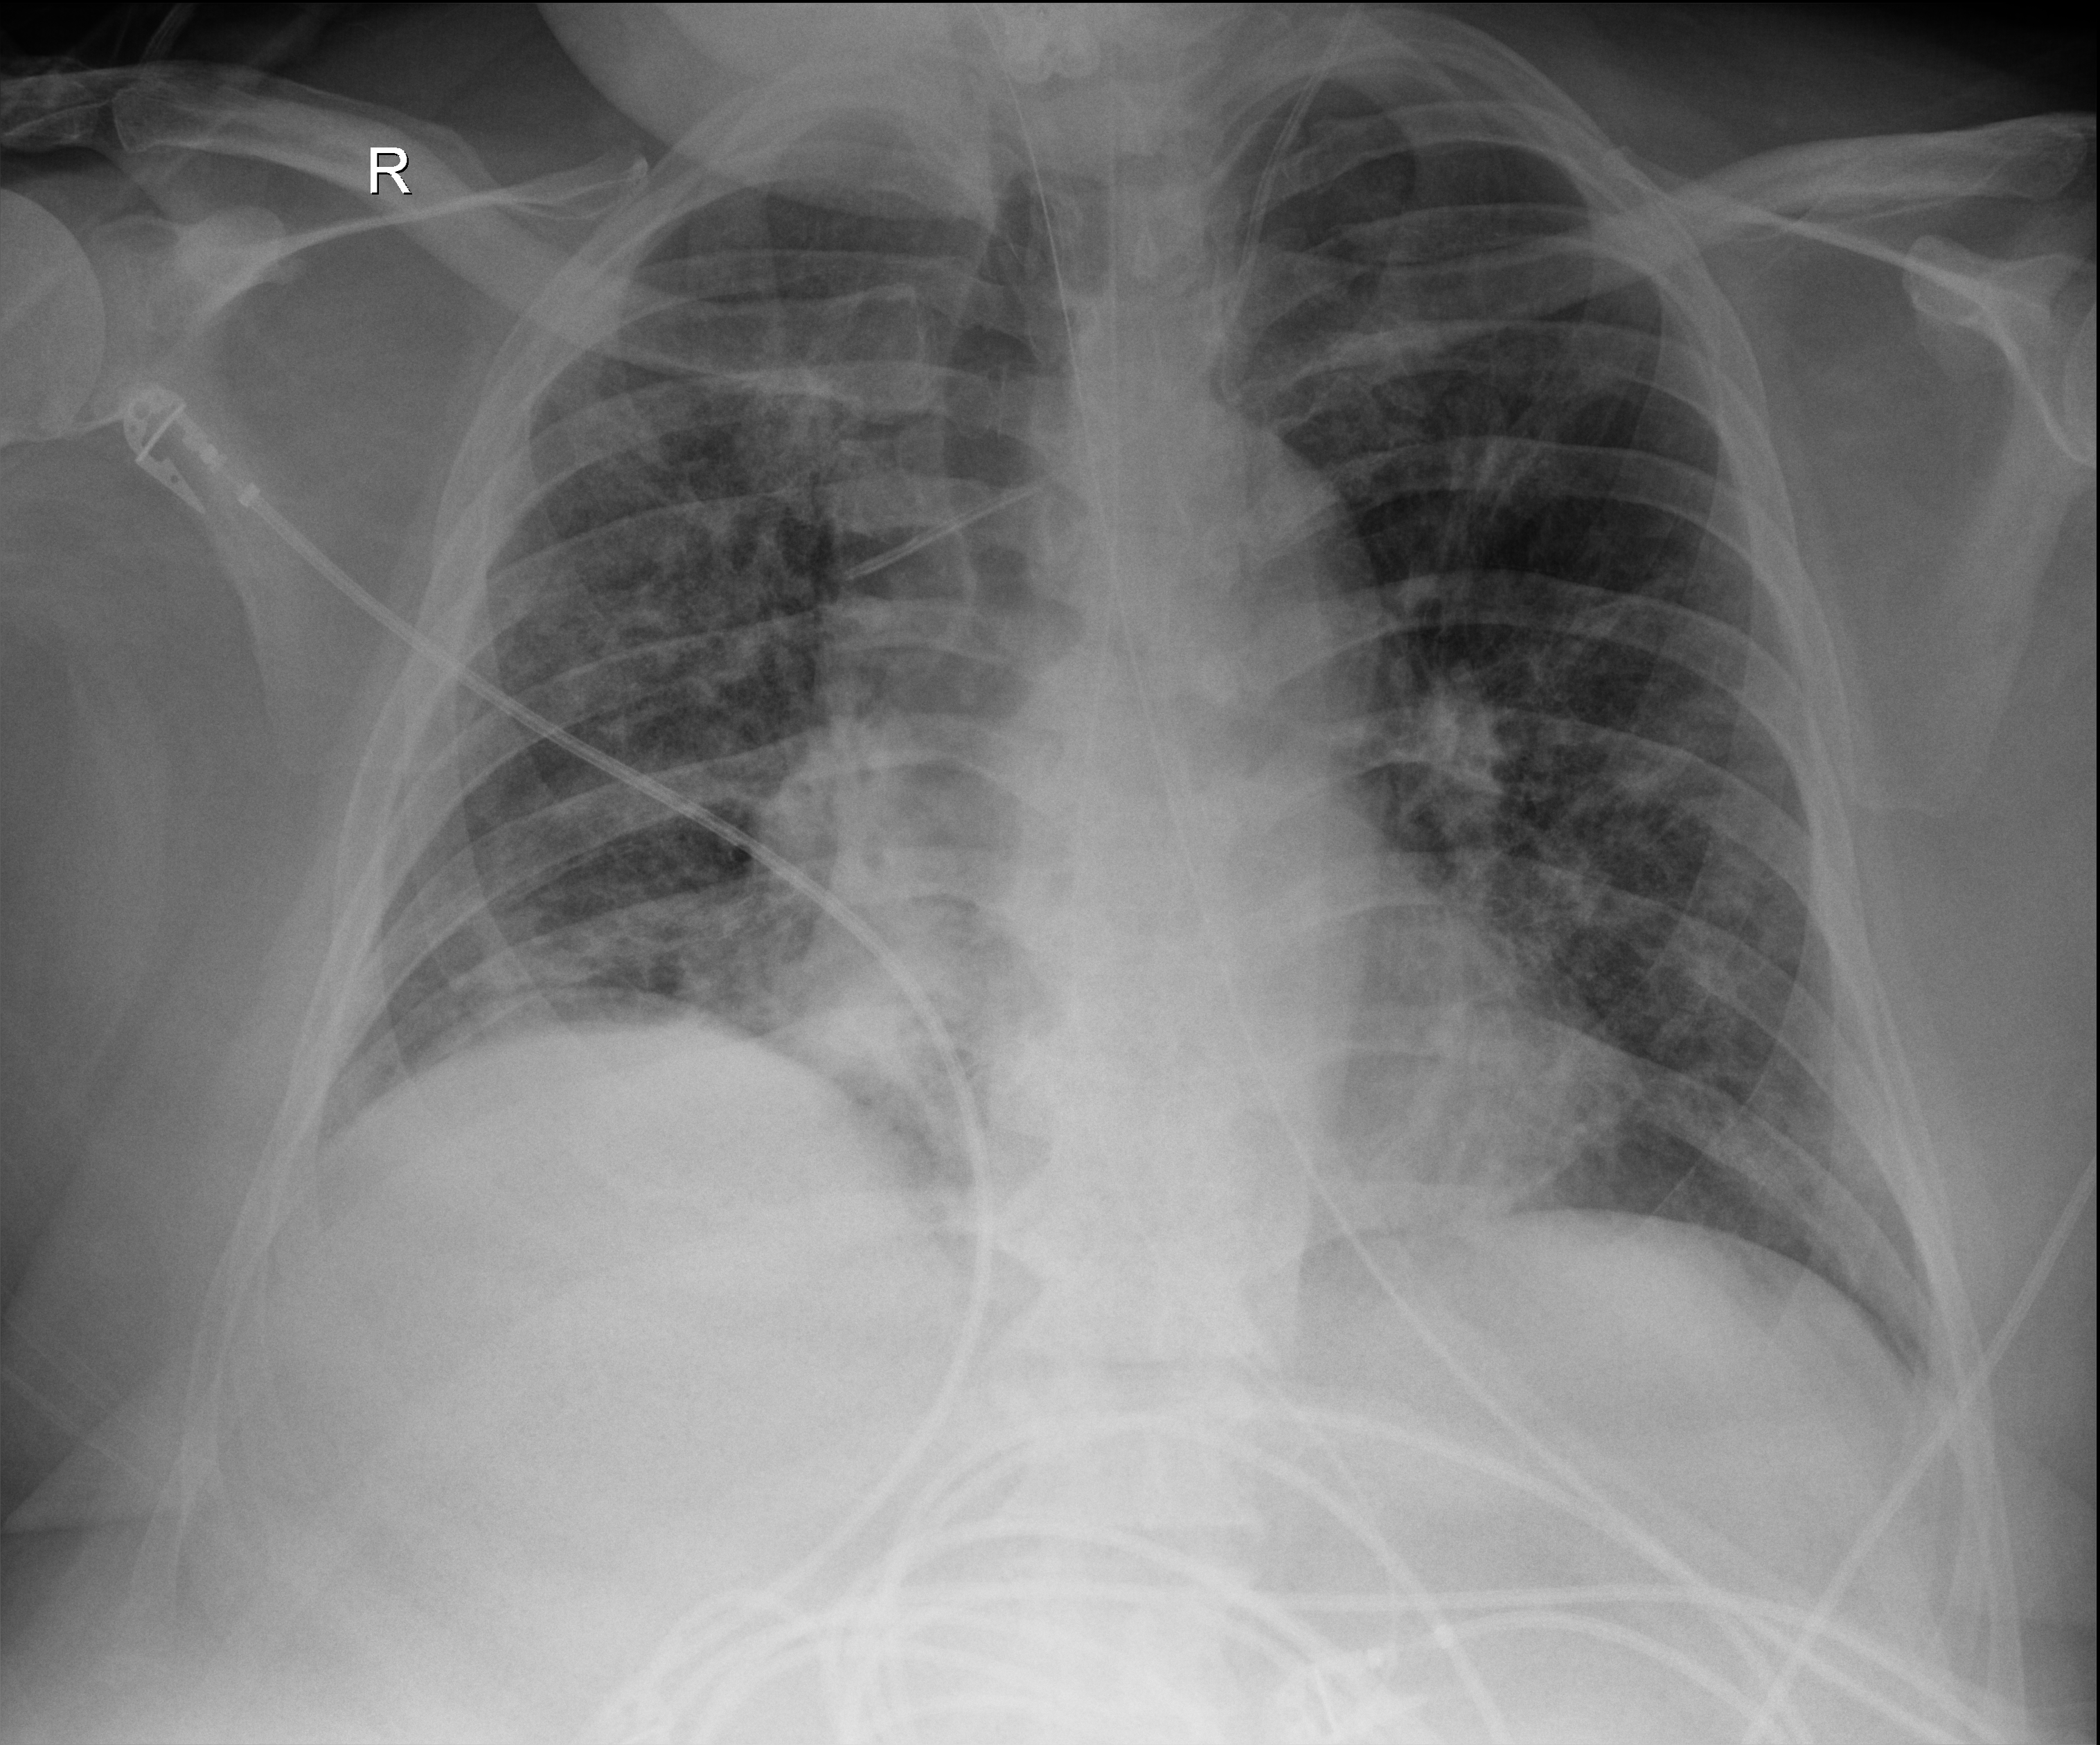
Chest X-ray (portable); anteroposterior (AP) projection. Patient hospitalised with COVID-19; male, aged 18–59 years.
Hospital-stay facts (about this admission, not read from this image; timing relative to this image not recorded):
- mechanically ventilated during this hospital stay: yes
- admitted to intensive care during this hospital stay: yes
- smoking status (admission record): never